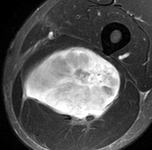
MRI of an extremity soft-tissue mass, one axial slice; slice 60 of 90 in the series (ordered by position); STIR; MR volume resampled by the dataset authors to the PET/CT grid (not the native acquisition matrix); 3.27 mm slice thickness; 152 × 150 image matrix. Male patient. From the clinical record (not read from this slice): histological type: undifferentiated pleomorphic liposarcoma; grade: high; site of the primary tumour: left thigh.
Annotated regions visible in this slice (expert contour drawn on MRI and transferred to this co-registered scan by the dataset authors):
- gross tumour volume including surrounding oedema: box from (x=20, y=46) to (x=122, y=127) px
- gross tumour volume (mass): (x=20, y=46)–(x=122, y=124)